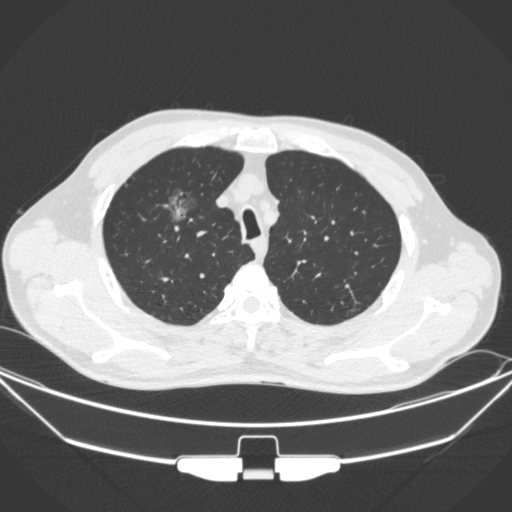
Chest CT, one axial slice. Slice 276 of 355 in the series (ordered by position). 120 kVp. Lung window (W 1500 / L -600 HU). 1 mm slice thickness. 512 × 512 image matrix. Patient: male, 67 years. From the clinical record (not read from this slice): clinical TNM (as recorded): T1c N0 M0; histopathological grade: G2.
Structures marked on this image (bounding box drawn by a radiologist):
- lung tumour (recorded histology: adenocarcinoma): bounding box (x1, y1, x2, y2) in pixels: (154, 183, 199, 233)